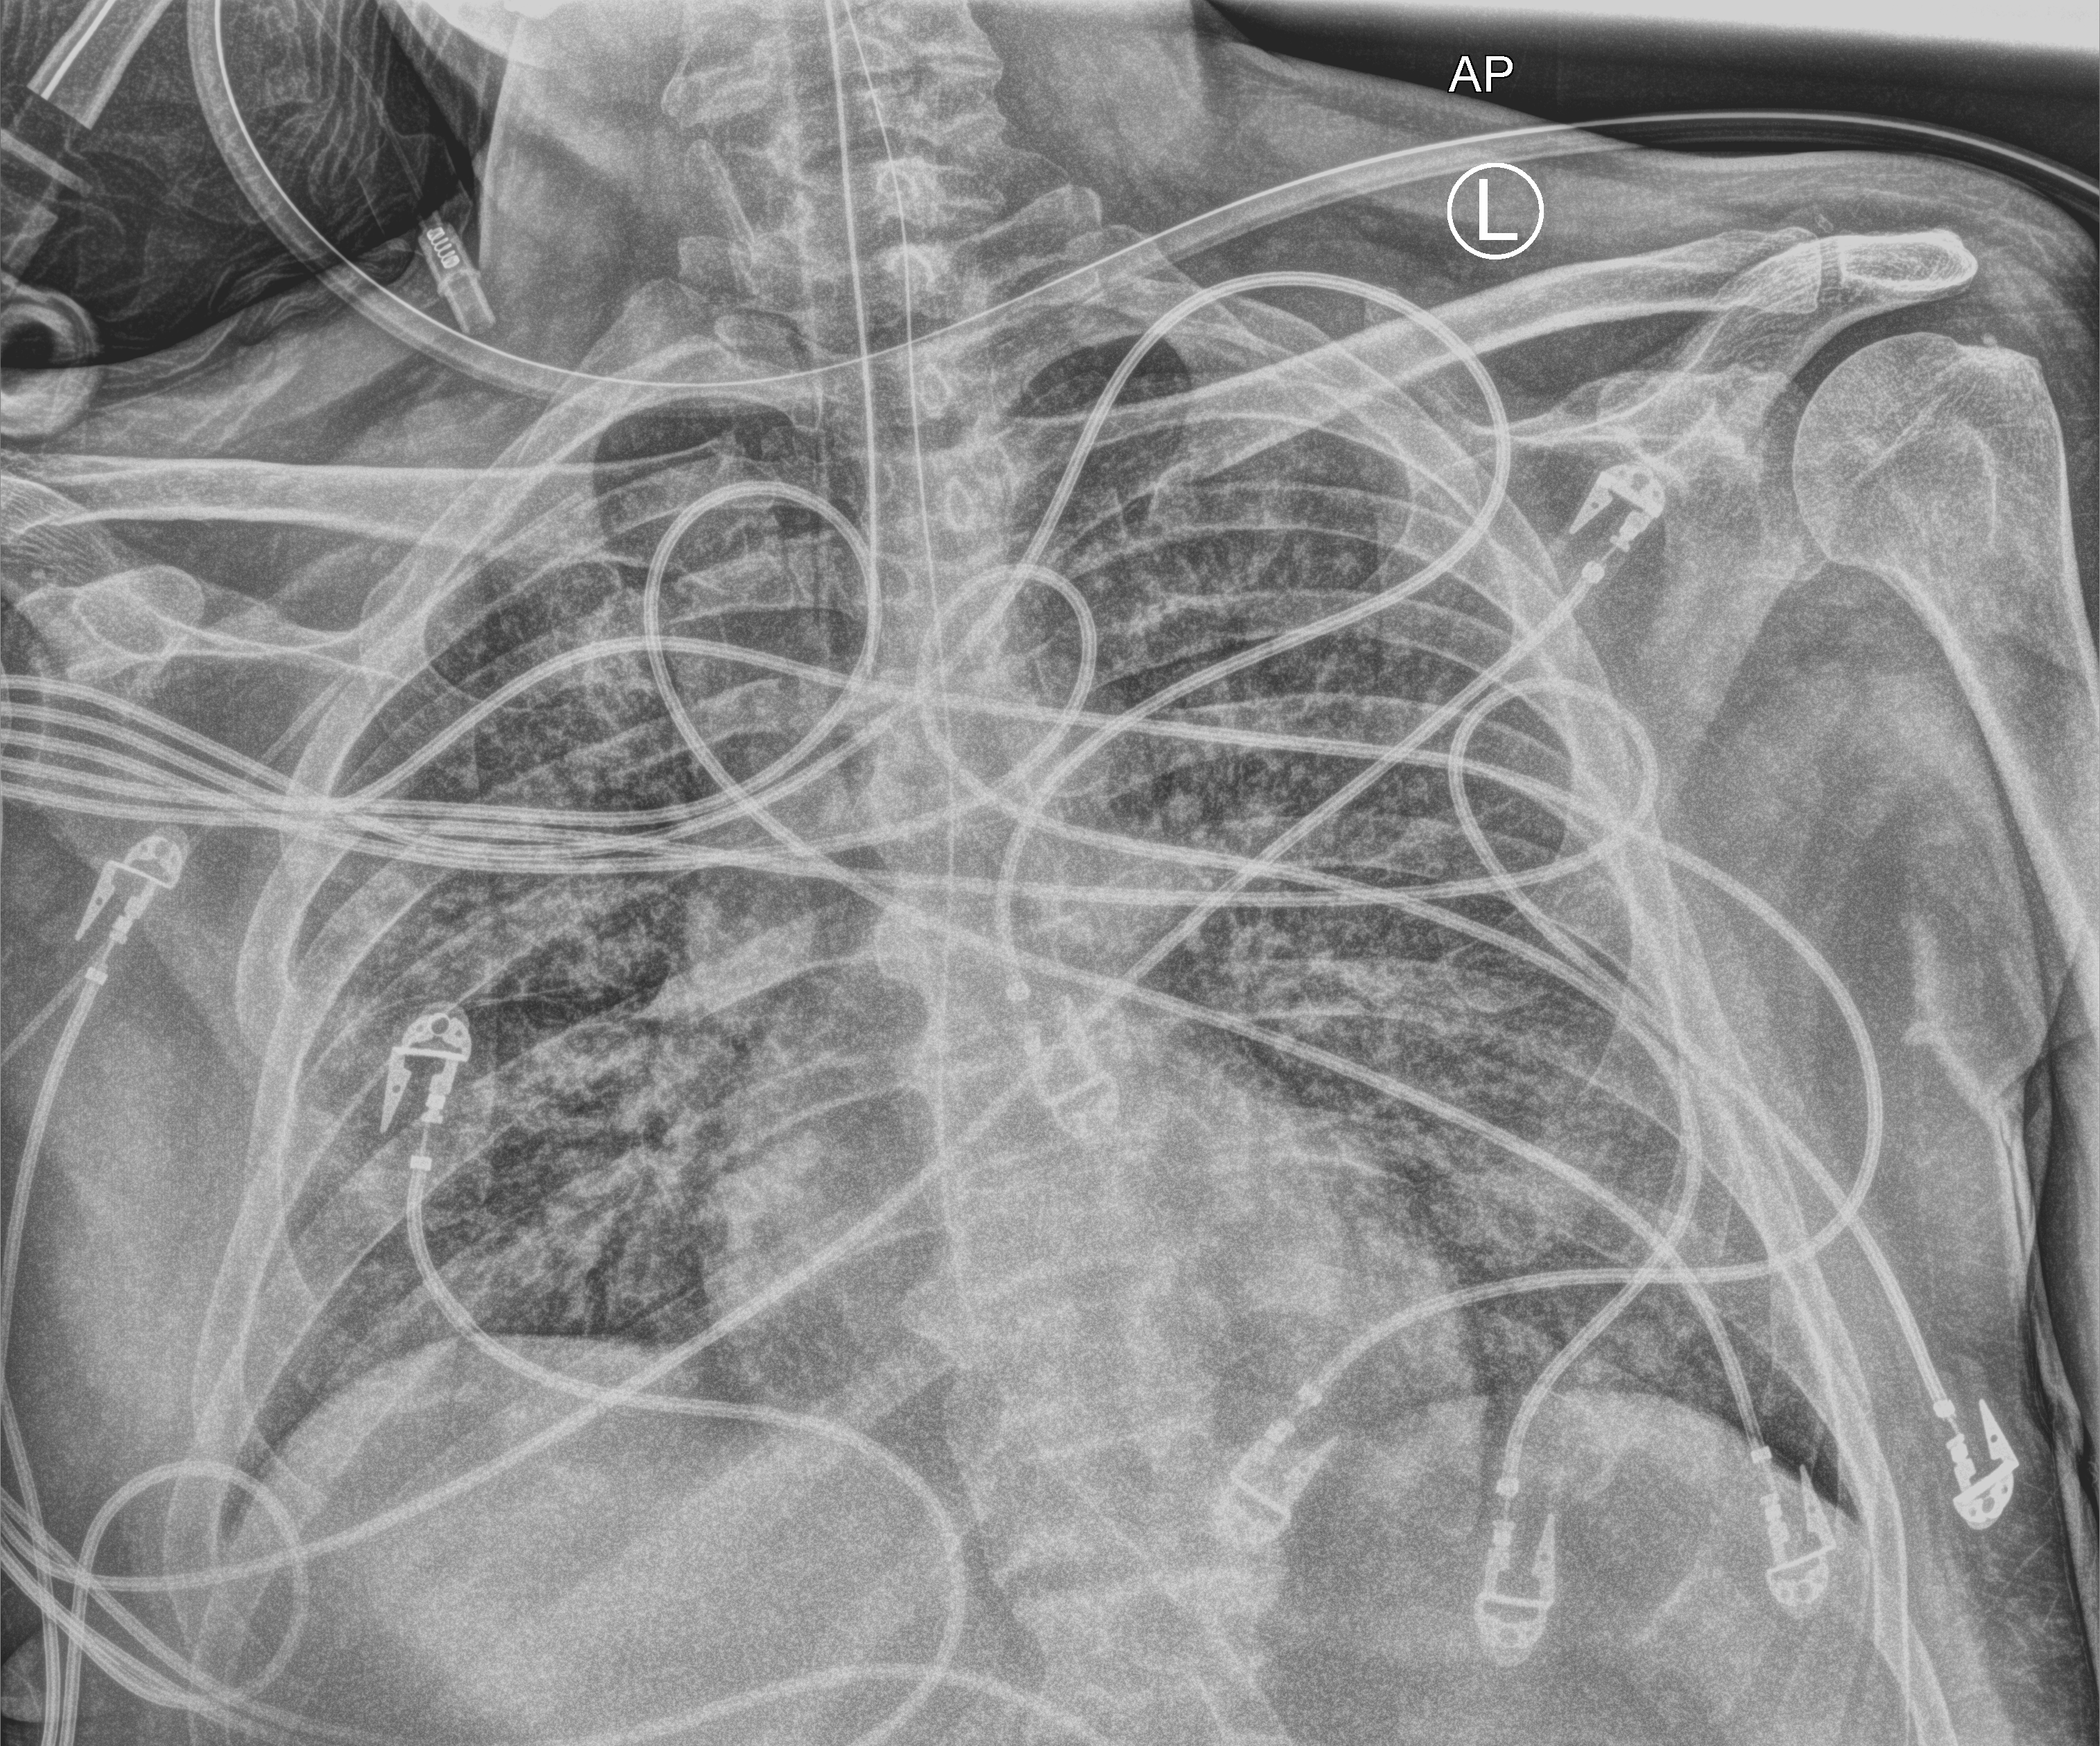
Portable chest radiograph; anteroposterior (AP) projection. Patient hospitalised with COVID-19; male, aged 60–74 years.
Admission-level facts for this patient (not findings on this image; timing relative to this image not recorded):
- admitted to intensive care during this hospital stay: yes
- mechanically ventilated during this hospital stay: yes